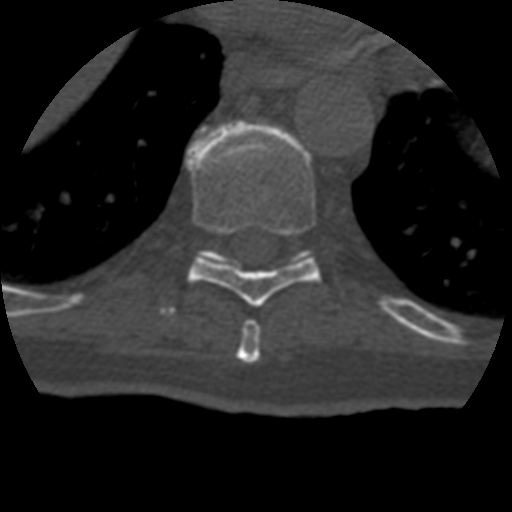
CT including the spine, one axial slice. Slice 236 of 399 in the series (ordered by position). Reconstruction kernel STANDARD. 120 kVp. Bone window (W 1800 / L 400 HU). 1.25 mm slice thickness. 512 × 512 image matrix. Patient age 69 years. From the clinical record (not read from this slice): primary cancer: prostate.
Structures marked on this image (semi-automatically segmented with operator editing):
- T10 vertebra: bounding box (x1, y1, x2, y2) in pixels: (200, 249, 311, 264)
- T8 vertebra: (236, 320, 261, 363)
- T9 vertebra: (187, 122, 320, 307)